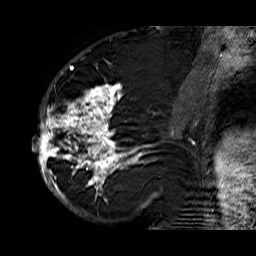
Breast MRI (dynamic contrast-enhanced), one sagittal slice; position 30 of 60 along the scan axis; dynamic contrast-enhanced series, time point 2 of 6 at this slice position (early post-contrast); 1.5 T; TE 6.3 ms, TR 32.9 ms; 4 mm slice thickness; 256 × 256 image matrix, field of view 200 × 200 mm. Female patient. Case-level facts recorded for this patient, not image findings: setting: breast cancer imaged before/during neoadjuvant chemotherapy; receptor status: HR-positive, HER2-negative.
Outlined on this slice (semi-automatic segmentation, software-assisted and operator-edited):
- analysis volume of interest (the breast-tissue region the enhancement analysis was run in; not a lesion): bounding box <33,74,176,210> (left, top, right, bottom; pixels)
- tumour enhancement mask (voxels above the 100 % enhancement threshold inside the analysis volume of interest): <33,74,174,210>